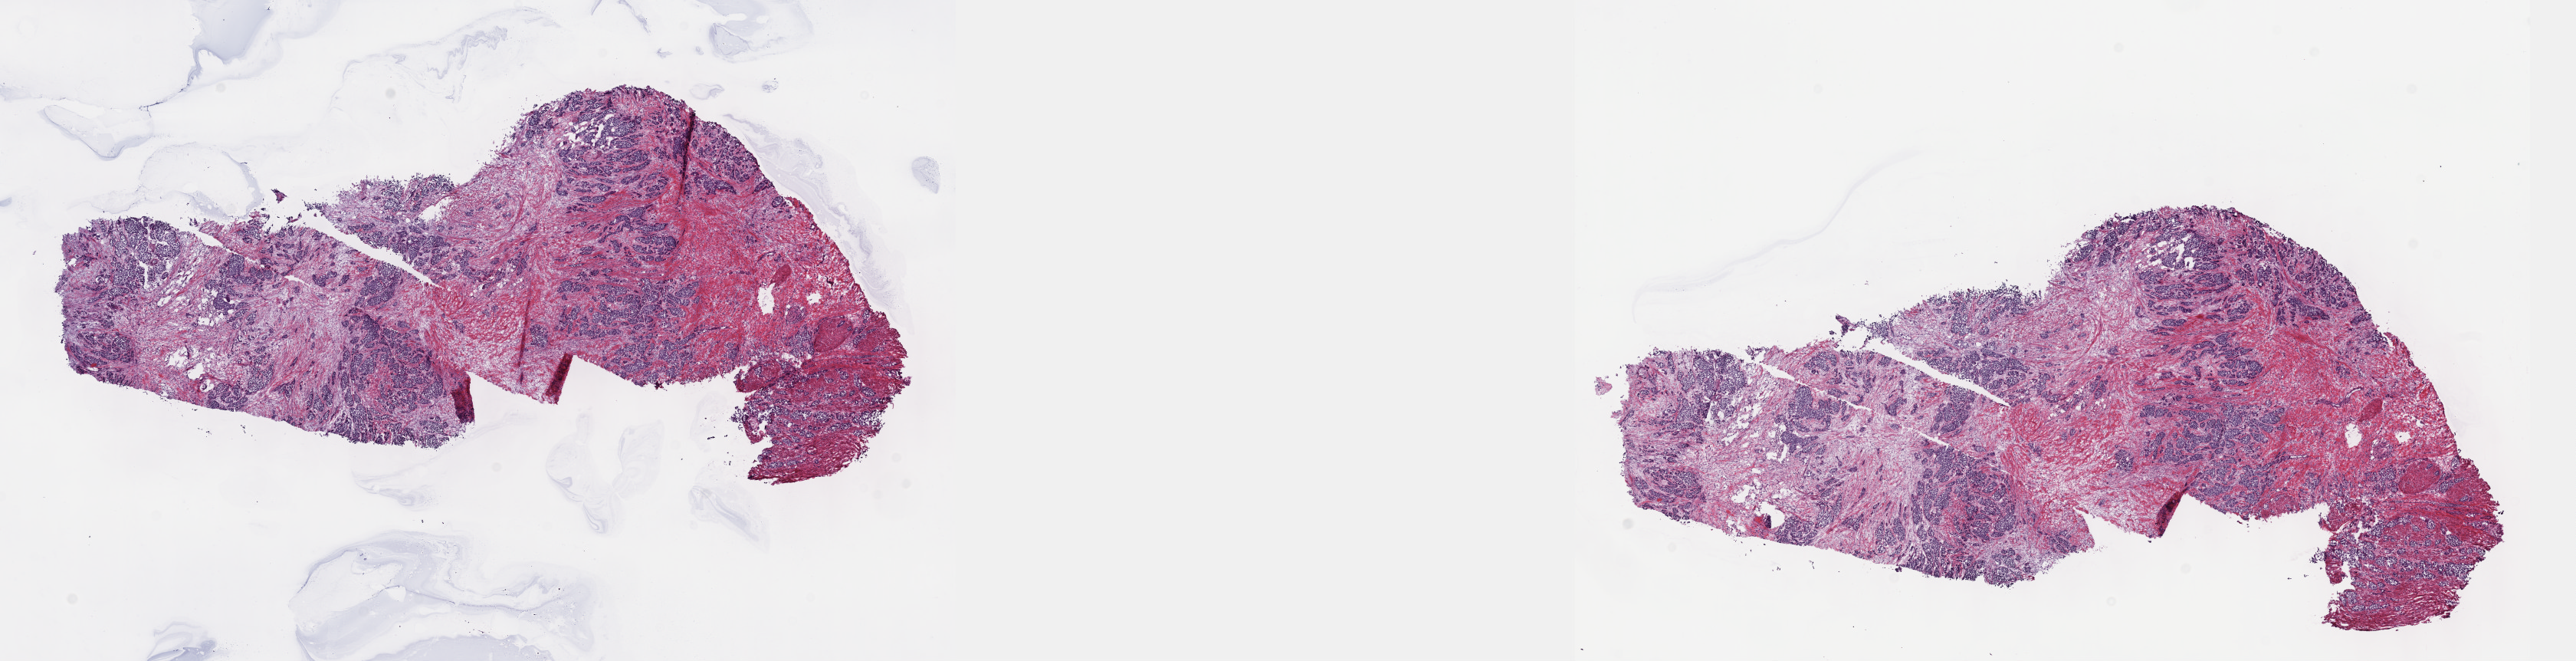
H&E-stained whole-slide image — low-resolution overview of the scanned area, about 27.2 x 7.0 mm. Frozen section from the top of the tissue portion. Primary tumour sample from the bladder. Patient: male, age at initial diagnosis 82 years. Histologic grade: high grade. Pathologist review of this section (percent, as recorded): tumour cells 70%, tumour nuclei 70%, normal cells 0%, stromal cells 28%, necrosis 2%. Infiltration values recorded for this section: lymphocyte infiltration 3%, monocyte infiltration 1%, neutrophil infiltration 5%.
* histologic diagnosis: Papillary transitional cell carcinoma
* lymph nodes positive (case pathology): 5 of 93 examined
* AJCC pathologic stage: IV
* TNM: T4a N2 M1